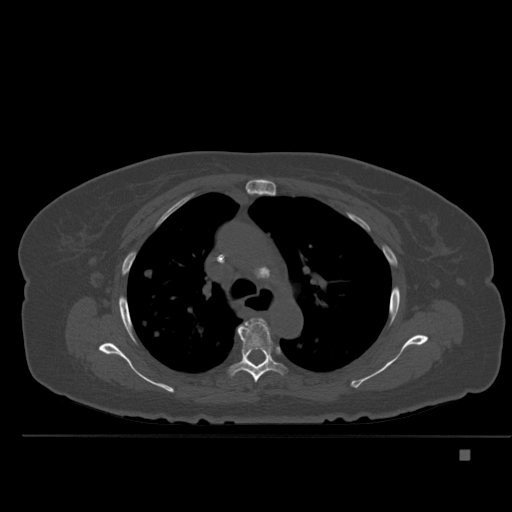
CT including the spine, one axial slice. Position 355 of 477 along the scan axis. Bone window (W 1800 / L 400 HU). 1.5 mm slice thickness. 512 × 512 image matrix, field of view 422 × 422 mm. Patient: female, 74 years. From the clinical record (not read from this slice): primary cancer: colon.
Annotated regions visible in this slice (semi-automatically segmented with operator editing):
- T4 vertebra: bounding box (x1, y1, x2, y2) in pixels: (251, 320, 263, 322)
- T5 vertebra: (230, 319, 285, 383)